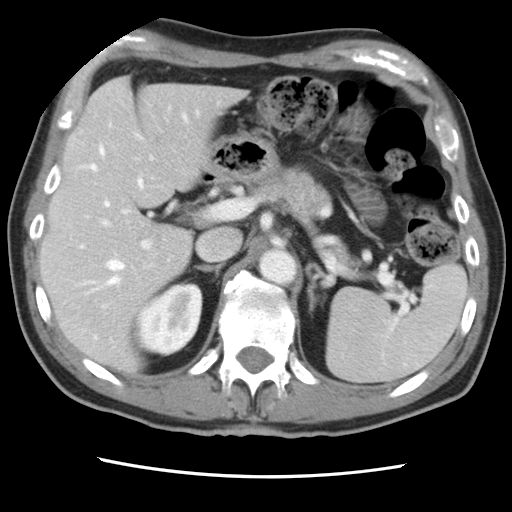
Contrast-enhanced abdominal CT, one axial slice; intravenous contrast given; soft-tissue window (W 400 / L 40 HU); 5 mm slice thickness; 512 × 512 image matrix. Male patient, age 69 years. Case-level facts recorded for this patient, not image findings: diagnosis: colorectal cancer liver metastases, imaged before liver resection; multiple liver metastases: yes; largest metastasis: 3.5 cm; disease in both lobes: no.
Annotated regions visible in this slice (manually delineated by an expert):
- hepatic veins: bounding box [x1, y1, x2, y2] px = [91, 115, 187, 338]
- liver: [43, 79, 240, 370]
- planned liver remnant (the part of the liver to remain after resection): [43, 137, 192, 370]
- portal vein (with intrahepatic branches): [79, 157, 231, 308]